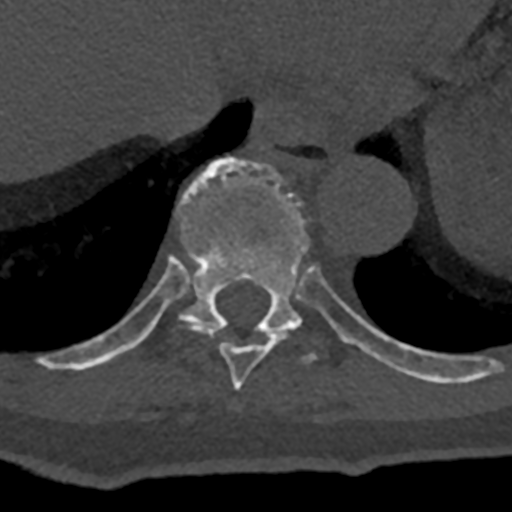
CT including the spine, one axial slice. Position 625 of 797 along the scan axis. Reconstruction kernel Br40s/3. Bone window (W 1800 / L 400 HU). 0.5 mm slice thickness. 512 × 512 image matrix, field of view 160 × 160 mm. Patient: male, 74 years. From the clinical record (not read from this slice): primary cancer: renal; vertebrae with lytic lesions (as recorded): T10, L1, L2, L3, L4, L5.
Structures marked on this image (semi-automatically segmented with operator editing):
- T10 vertebra: bounding box [x1, y1, x2, y2] px = [70, 157, 432, 382]
- T9 vertebra: [178, 319, 293, 390]